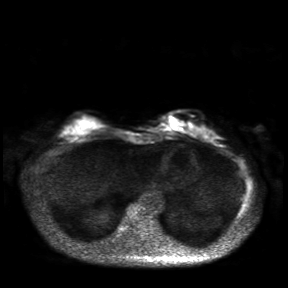
Breast MRI, one axial slice; slice 7 of 30 in the series (ordered by position); diffusion-weighted series; image 2 of 4 stored at this slice position (different b-values; order by instance number); 3 T; 4 mm slice thickness; 288 × 288 image matrix, field of view 360 × 360 mm. Female patient.
Outlined on this slice (outlined manually by an expert reader):
- tumour on diffusion-weighted imaging: box from (x=170, y=119) to (x=177, y=127) px